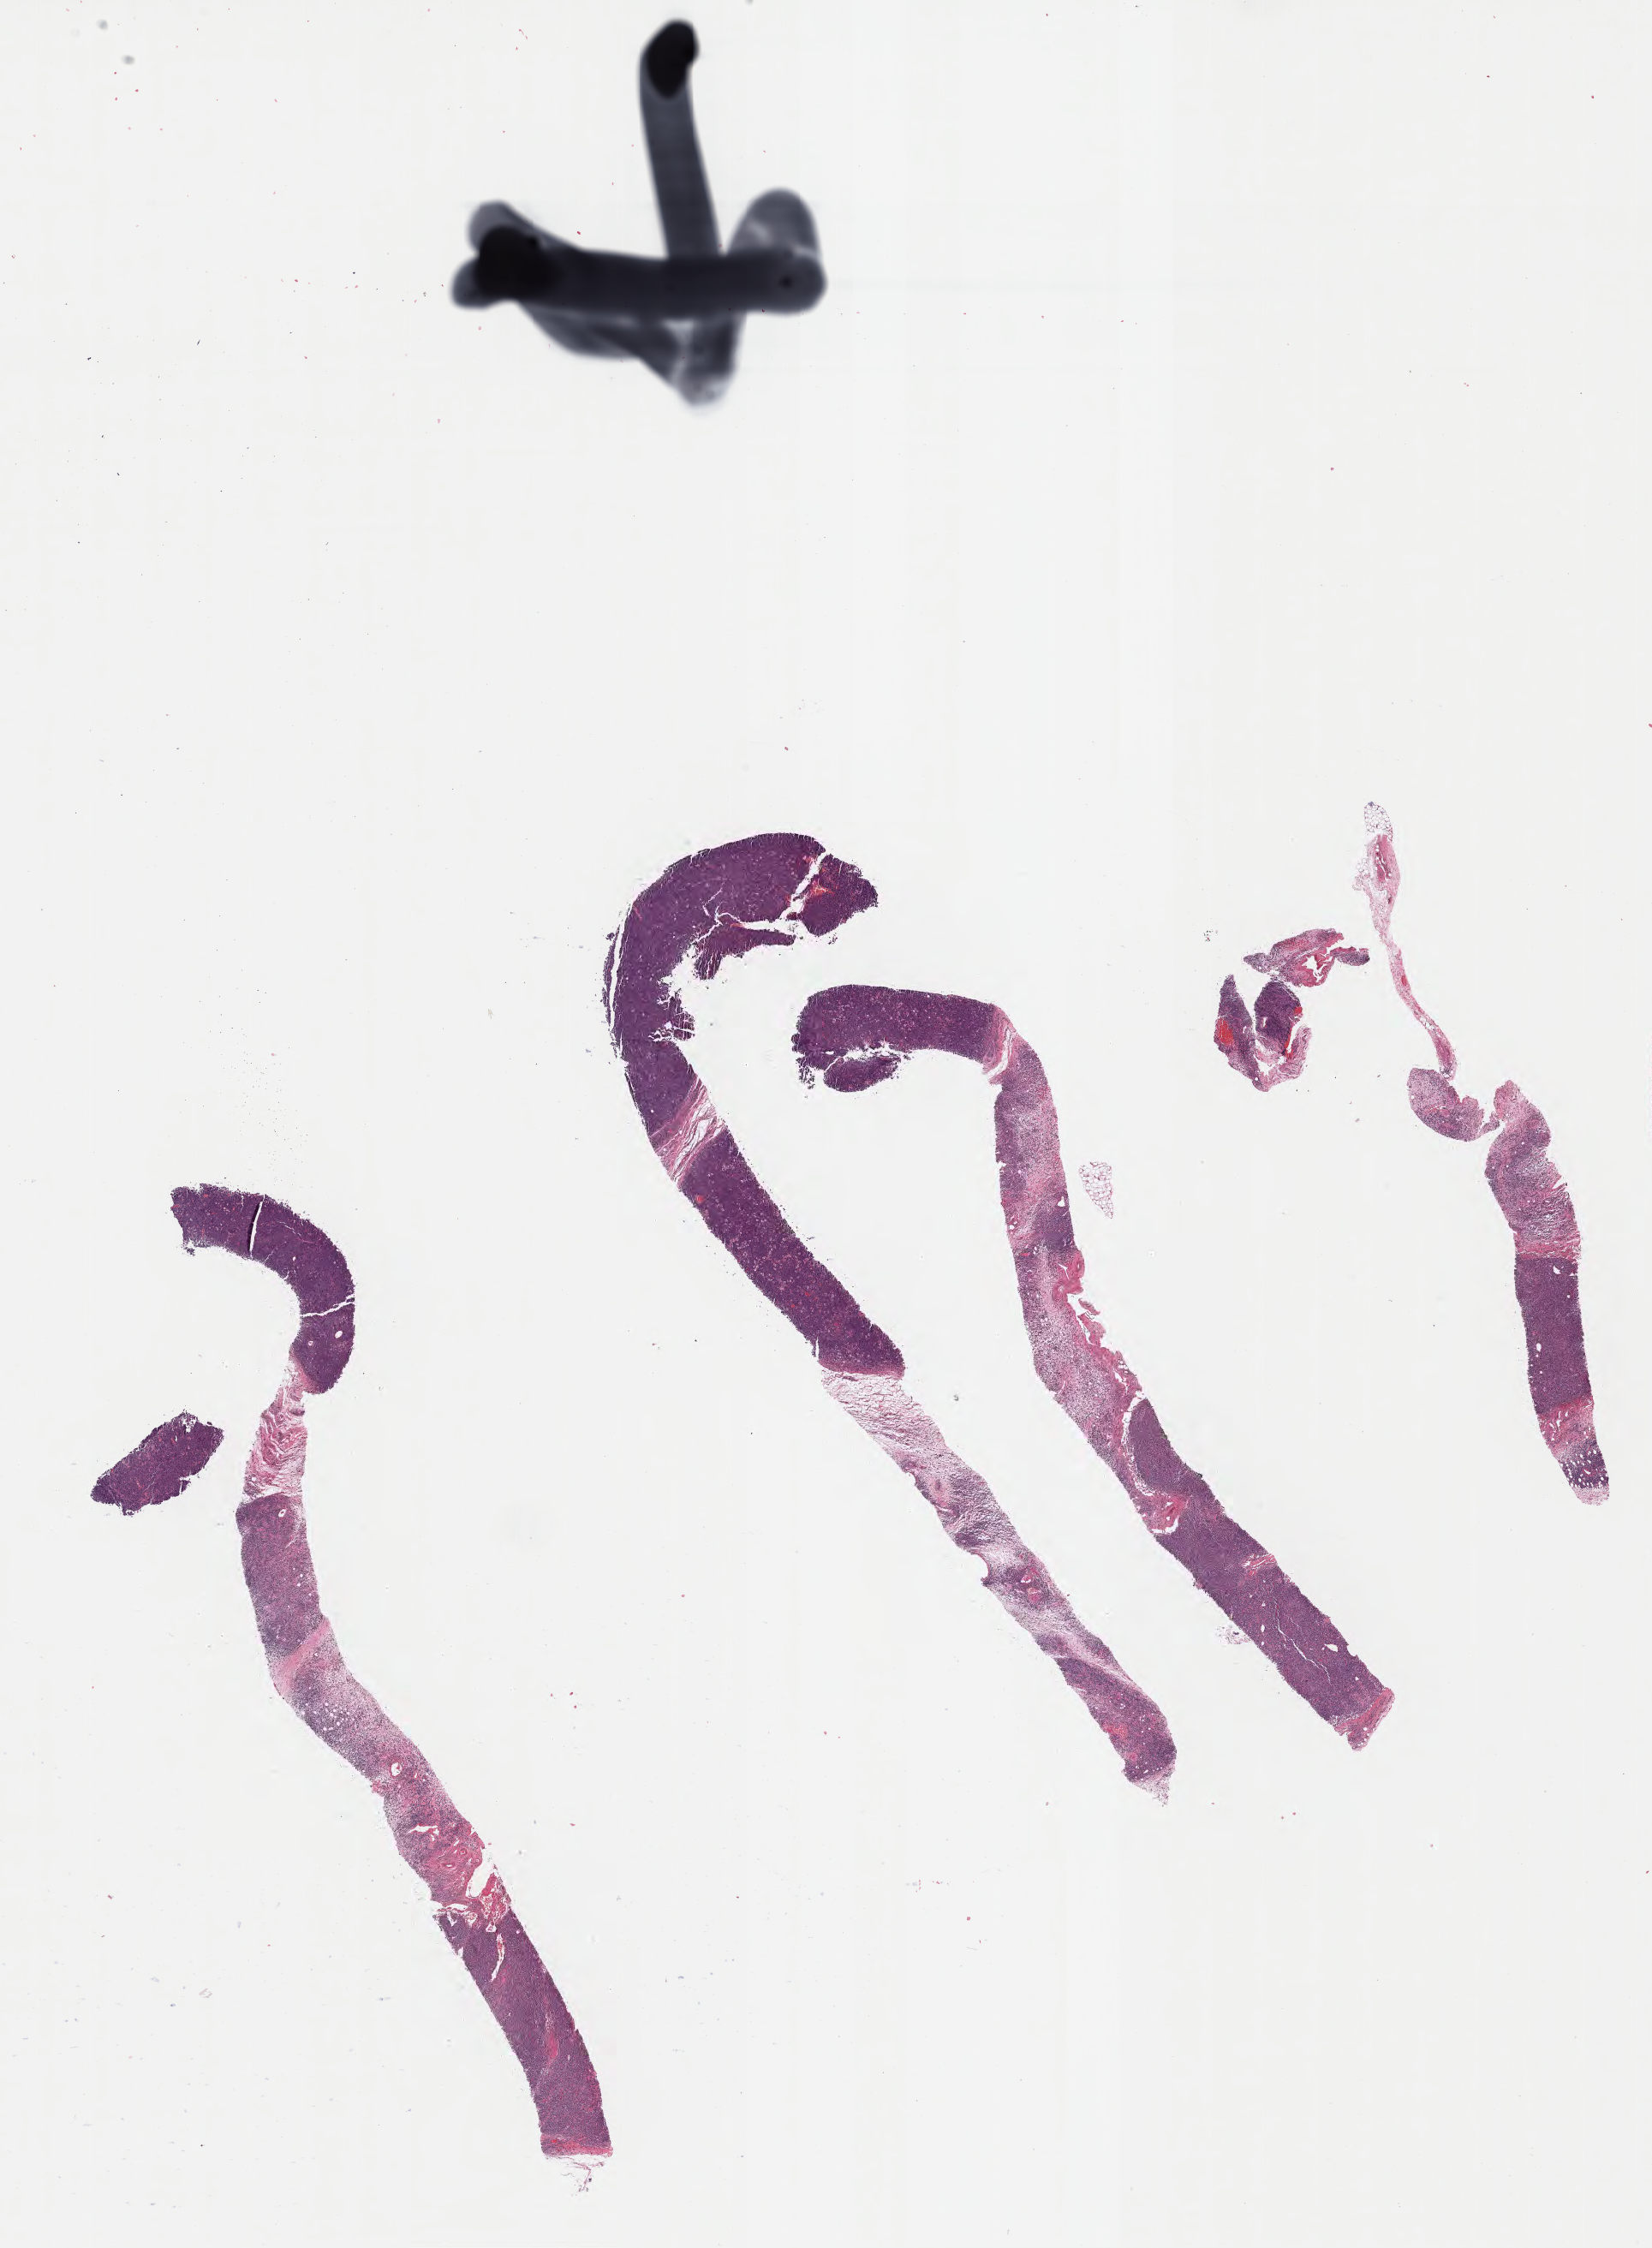
Digitized haematoxylin and eosin-stained section, low-resolution overview of the scanned area, about 15.6 x 21.2 mm; tumor tissue. Patient: male, 47 years old.
Diagnosis: Burkitt lymphoma, NOS.